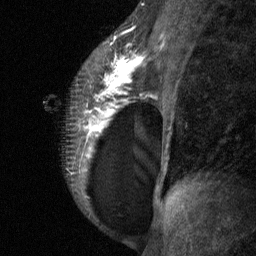
Breast MRI (dynamic contrast-enhanced), one sagittal slice. Position 43 of 64 along the scan axis. Dynamic contrast-enhanced study with each time point stored as its own series, time point 2 of 3 at this slice position (early post-contrast, ordered by acquisition time). 1.5 T. TE 4.8 ms, TR 27 ms. 256 × 256 image matrix, field of view 180 × 180 mm. Patient: female, 34 years. Case-level facts recorded for this patient, not image findings: setting: breast cancer imaged before/during neoadjuvant chemotherapy; receptor status: HR-positive, HER2-negative.
Outlined on this slice (semi-automatically segmented with operator editing):
- analysis volume of interest (the breast-tissue region the enhancement analysis was run in; not a lesion): bounding box [x1, y1, x2, y2] px = [43, 23, 157, 197]
- tumour enhancement mask (voxels above the 90 % enhancement threshold inside the analysis volume of interest): [79, 37, 146, 156]